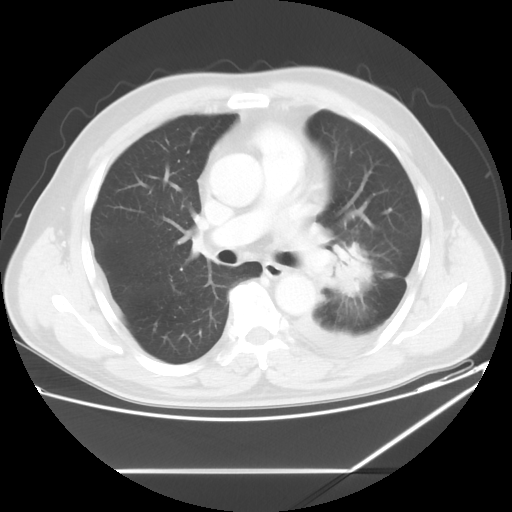
Chest CT, one axial slice. Position 34 of 60 along the scan axis. Reconstruction kernel STANDARD. Lung window (W 1500 / L -600 HU). 512 × 512 image matrix, field of view 395 × 395 mm. Patient: male, 62 years. From the clinical record (not read from this slice): clinical TNM (as recorded): T3 N0 M1.
Annotated regions visible in this slice (bounding box drawn by a radiologist):
- lung tumour (recorded histology: adenocarcinoma): box from (x=331, y=240) to (x=367, y=298) px
- lung tumour (recorded histology: adenocarcinoma): (x=337, y=248)–(x=383, y=301)